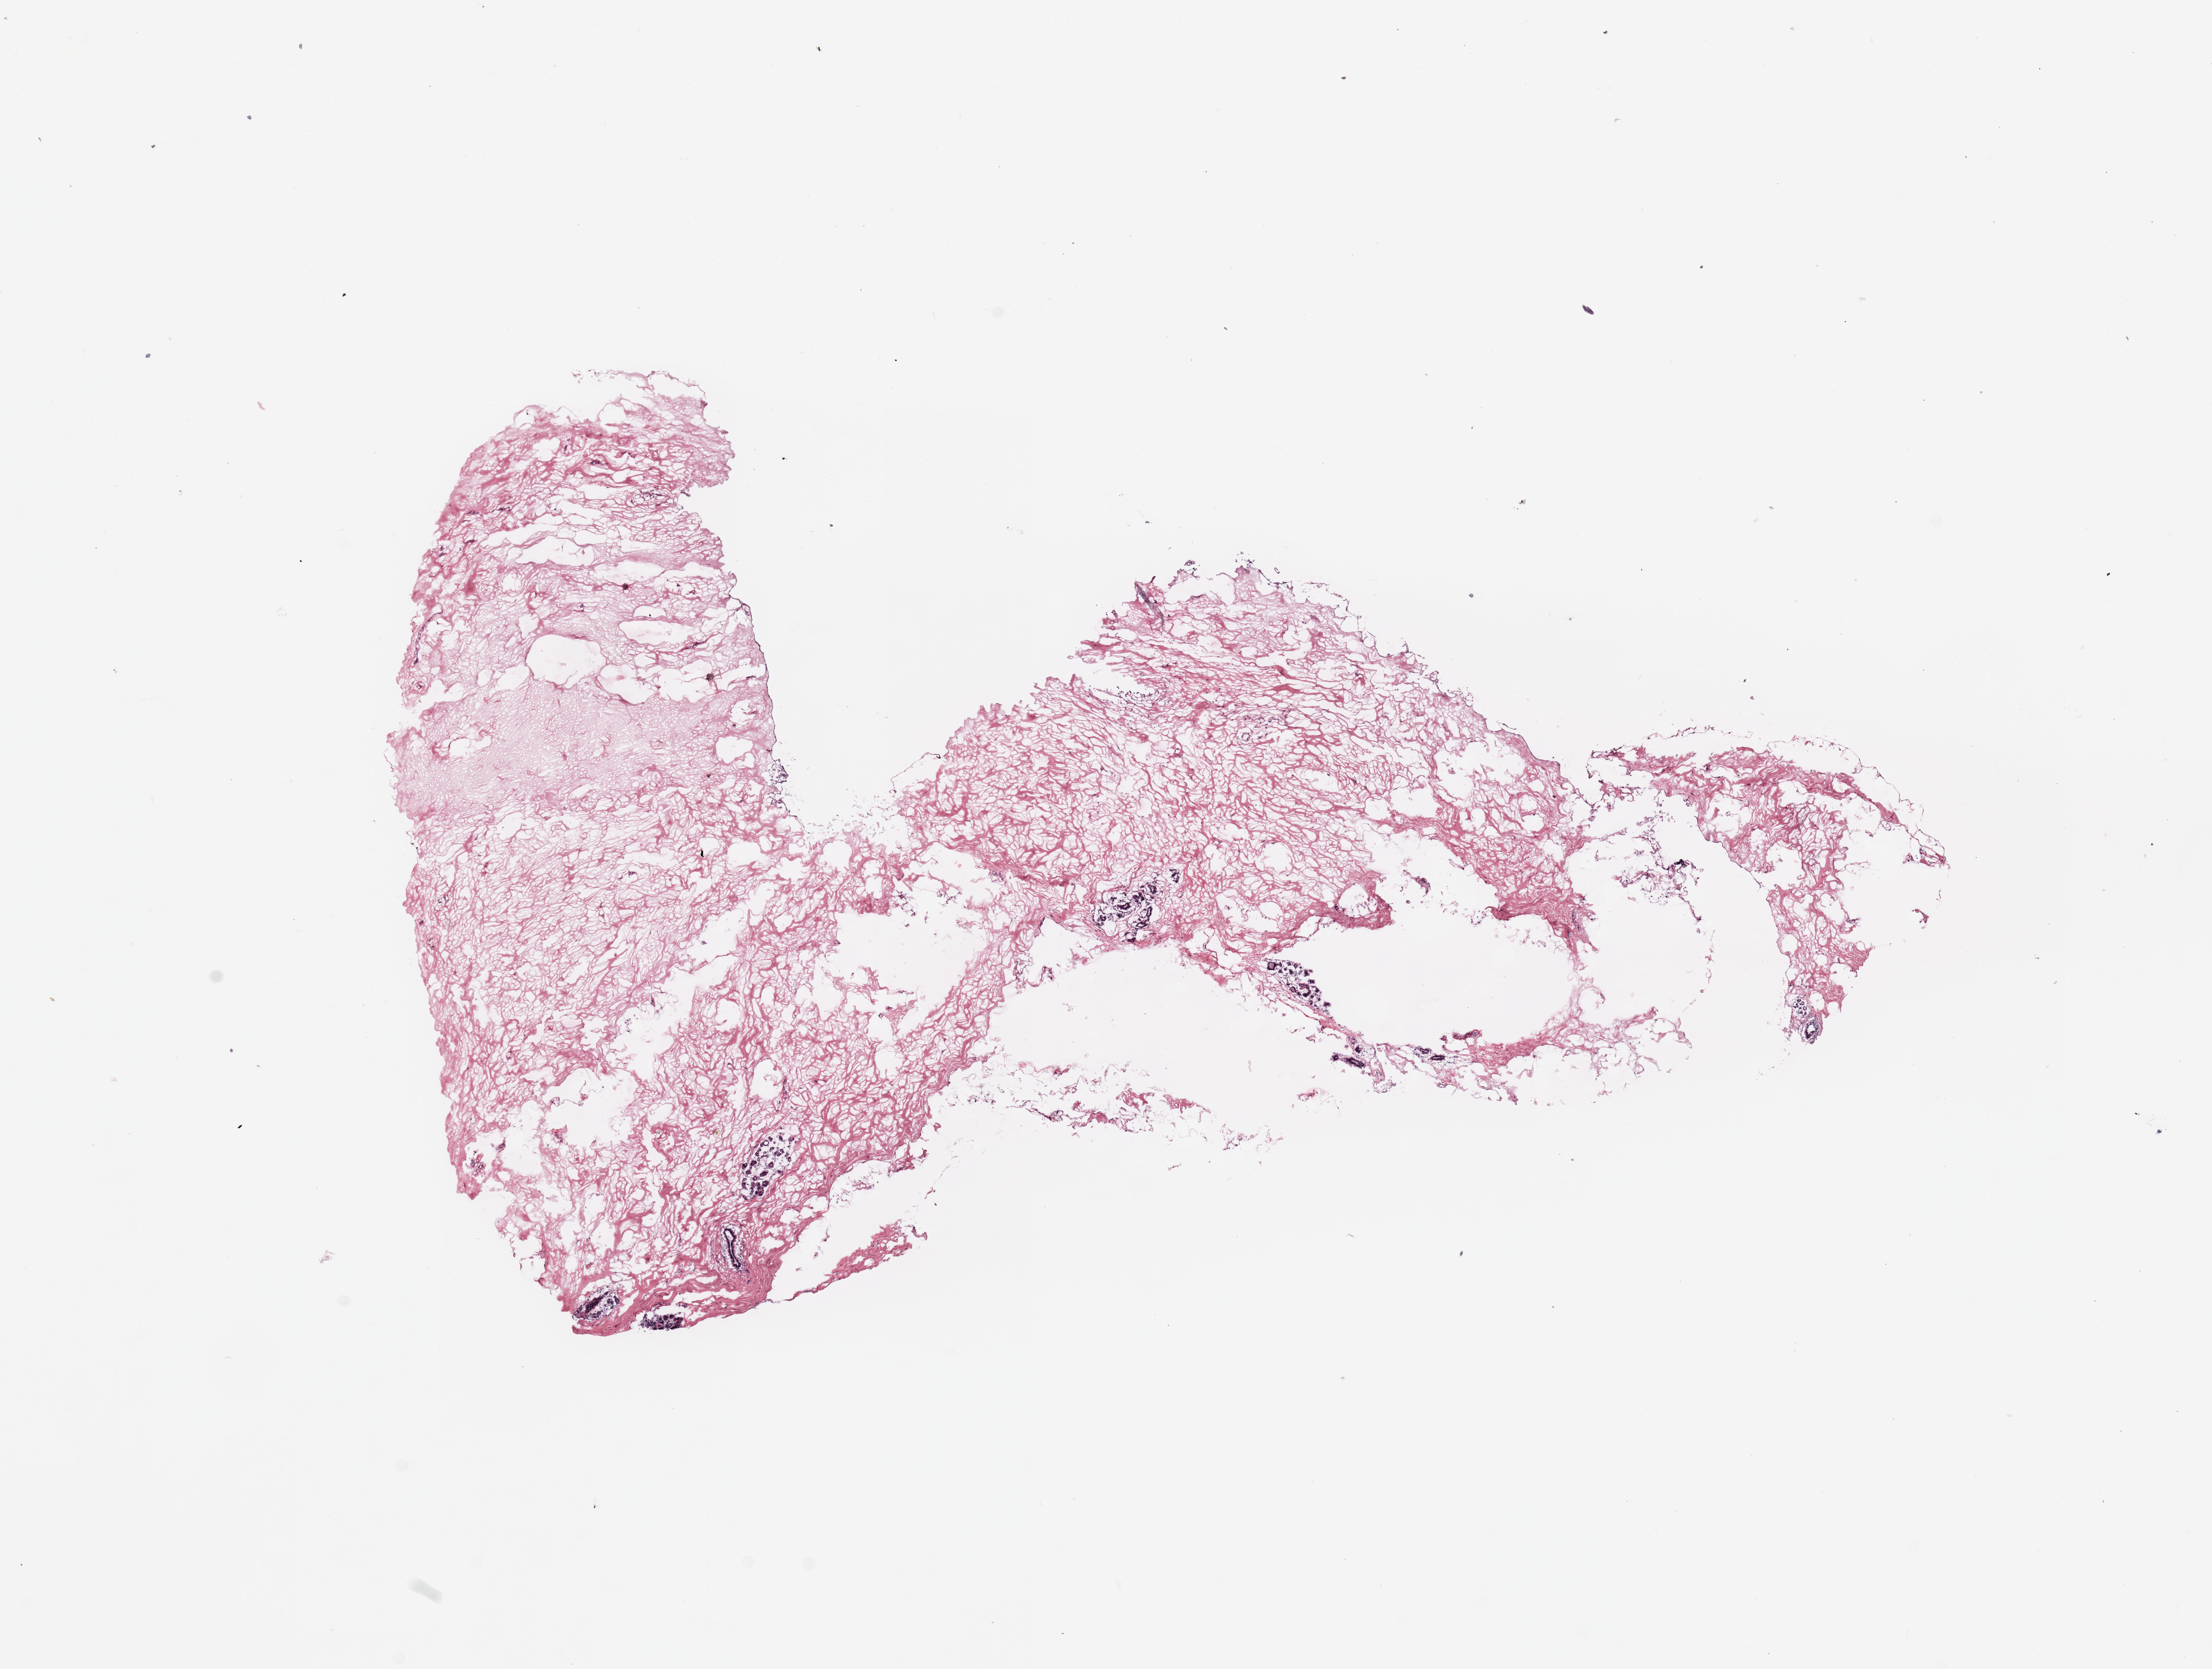
Whole-slide histology image, H&E, shown as a low-resolution overview of the whole scanned area (about 14.8 x 11.1 mm, slide scanned at 20x). Breast, tumour tissue. Patient: female, age 61 years.
- AJCC pathologic stage: IIA
- histologic diagnosis: Infiltrating duct carcinoma, NOS